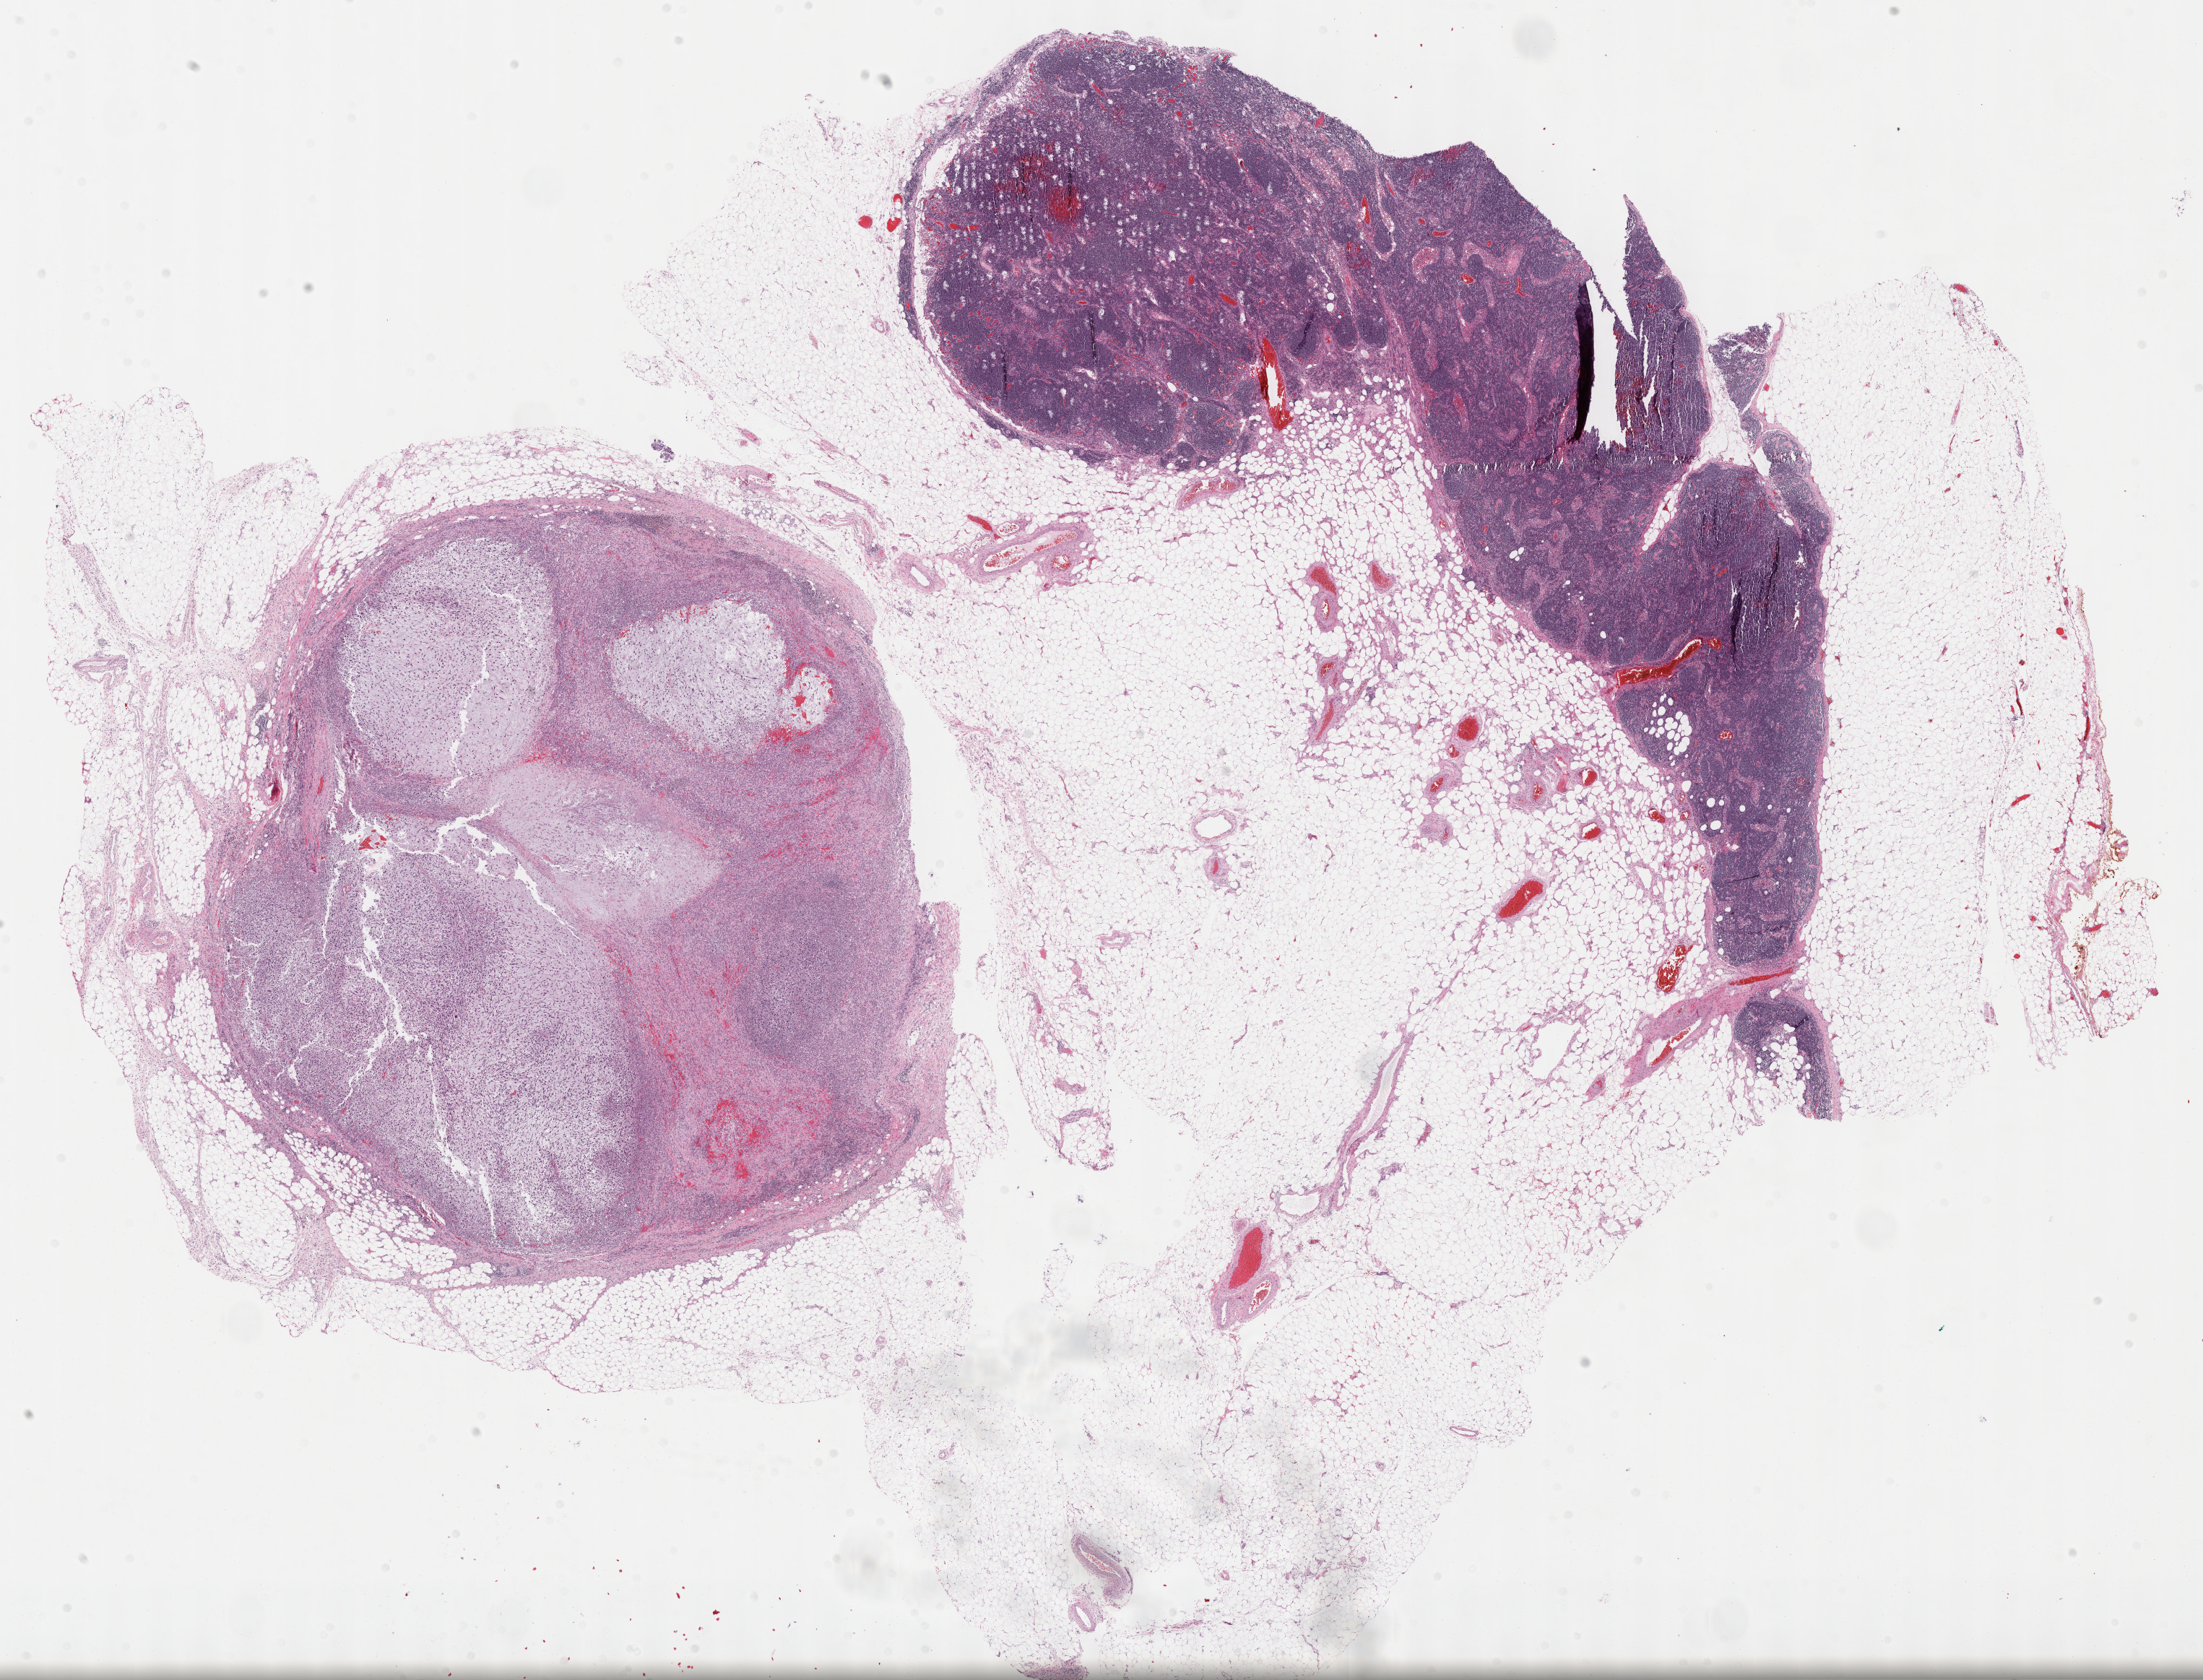
Digitized Hematoxylin and eosin (H&E) stained tissue section (whole slide), shown as a low-resolution overview of the whole scanned area (about 24.7 x 18.8 mm, acquisition: 40x scan); formalin-fixed paraffin-embedded (FFPE) diagnostic section; connective, subcutaneous and other soft tissues, primary tumour sample. Male patient; age at initial diagnosis 60 years.
• pathologic diagnosis: Fibromyxosarcoma (connective, subcutaneous and other soft tissues of thorax)